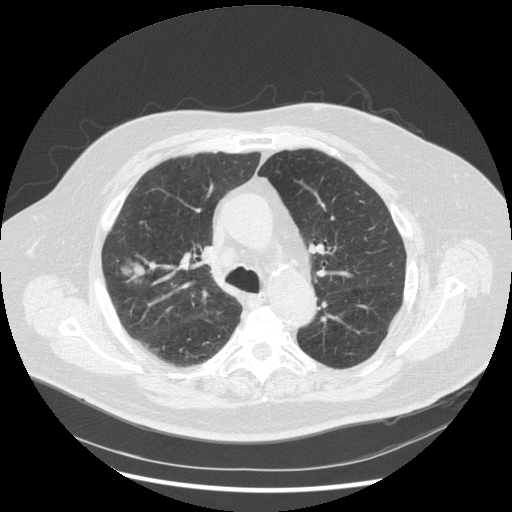
Axial slice from a low-dose chest CT screening exam. Third screening round (two years after baseline). Lung window (W 1500 / L -600 HU). 2.5 mm slice thickness. Male participant, aged 72 years at enrolment. Former smoker at enrolment.
Lesion marked by an expert reader, box from (x=99, y=249) to (x=156, y=297) px. The exam's reader record, not a measurement of the box and not confirmed to be the same lesion: non-calcified nodule or mass ≥4 mm, right upper lobe, 31 × 31 mm, poorly defined margins, soft tissue attenuation, pre-existing on the prior screen: no. Lung cancer was diagnosed 70 days after this screen: squamous cell carcinoma, NOS, right upper lobe, poorly differentiated (G3), stage IIIA (AJCC 6th edition), 19 mm at pathology.